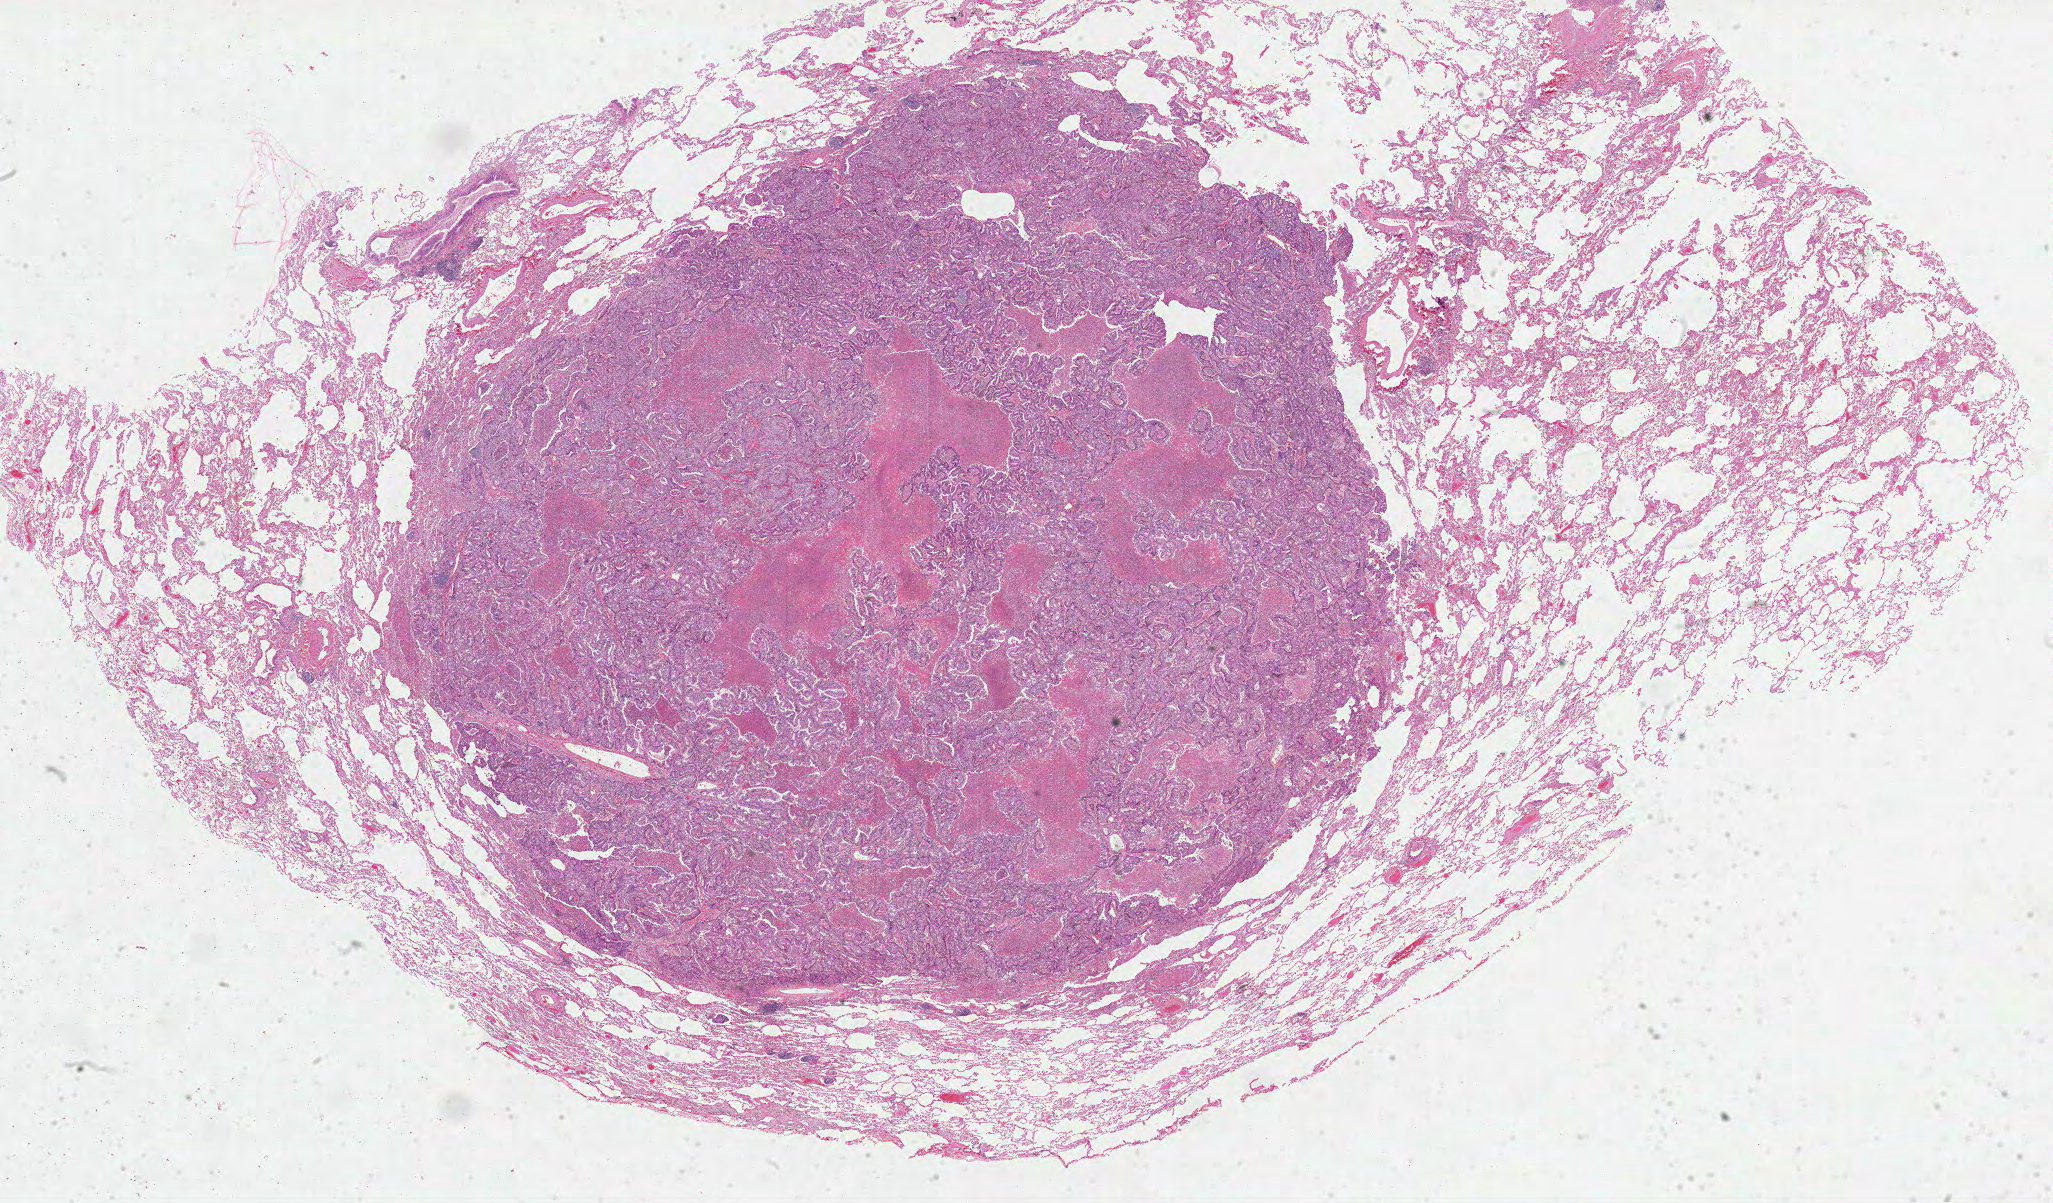
Digitized Hematoxylin and eosin (H&E) stained tissue section (whole slide), low-resolution overview of the scanned area, about 33.1 x 19.4 mm; formalin-fixed paraffin-embedded (FFPE) diagnostic section; sample: primary tumour, lung. Female patient; age at initial diagnosis 60 years.
- AJCC pathologic stage: IA (6th edition)
- TNM: T1 NX M0
- pathologic diagnosis: Adenocarcinoma with mixed subtypes (upper lobe, lung)
- laterality: left